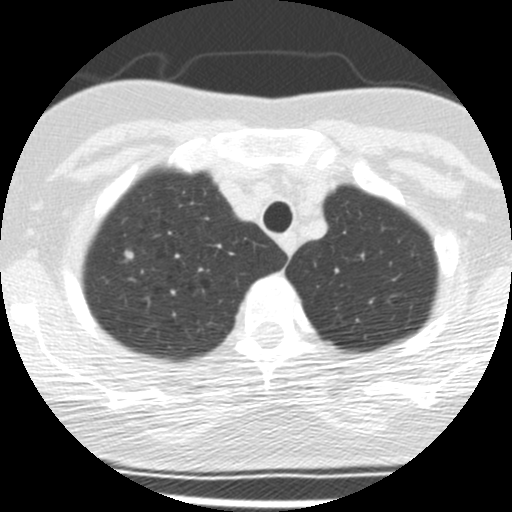
Low-dose screening chest CT, one axial slice; slice 155 of 190 in the series (ordered by position); reconstruction kernel STANDARD; lung window (W 1500 / L -600 HU); 2.5 mm slice thickness; 512 × 512 image matrix.
Structures marked on this image (manually delineated by an expert):
- lesion 1 (tumor, upper lobe of right lung): bounding box <125,250,134,259> (left, top, right, bottom; pixels)